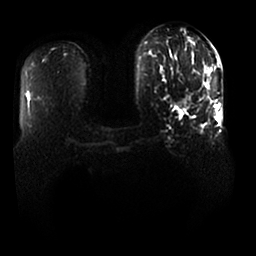
Breast MRI, one axial slice; position 7 of 25 along the scan axis; diffusion-weighted series; image 2 of 4 stored at this slice position (different b-values; order by instance number); 1.5 T; 256 × 256 image matrix, field of view 370 × 370 mm. Female patient.
Outlined on this slice (outlined manually by an expert reader):
- tumour on diffusion-weighted imaging: bounding box [x1, y1, x2, y2] px = [179, 69, 211, 108]